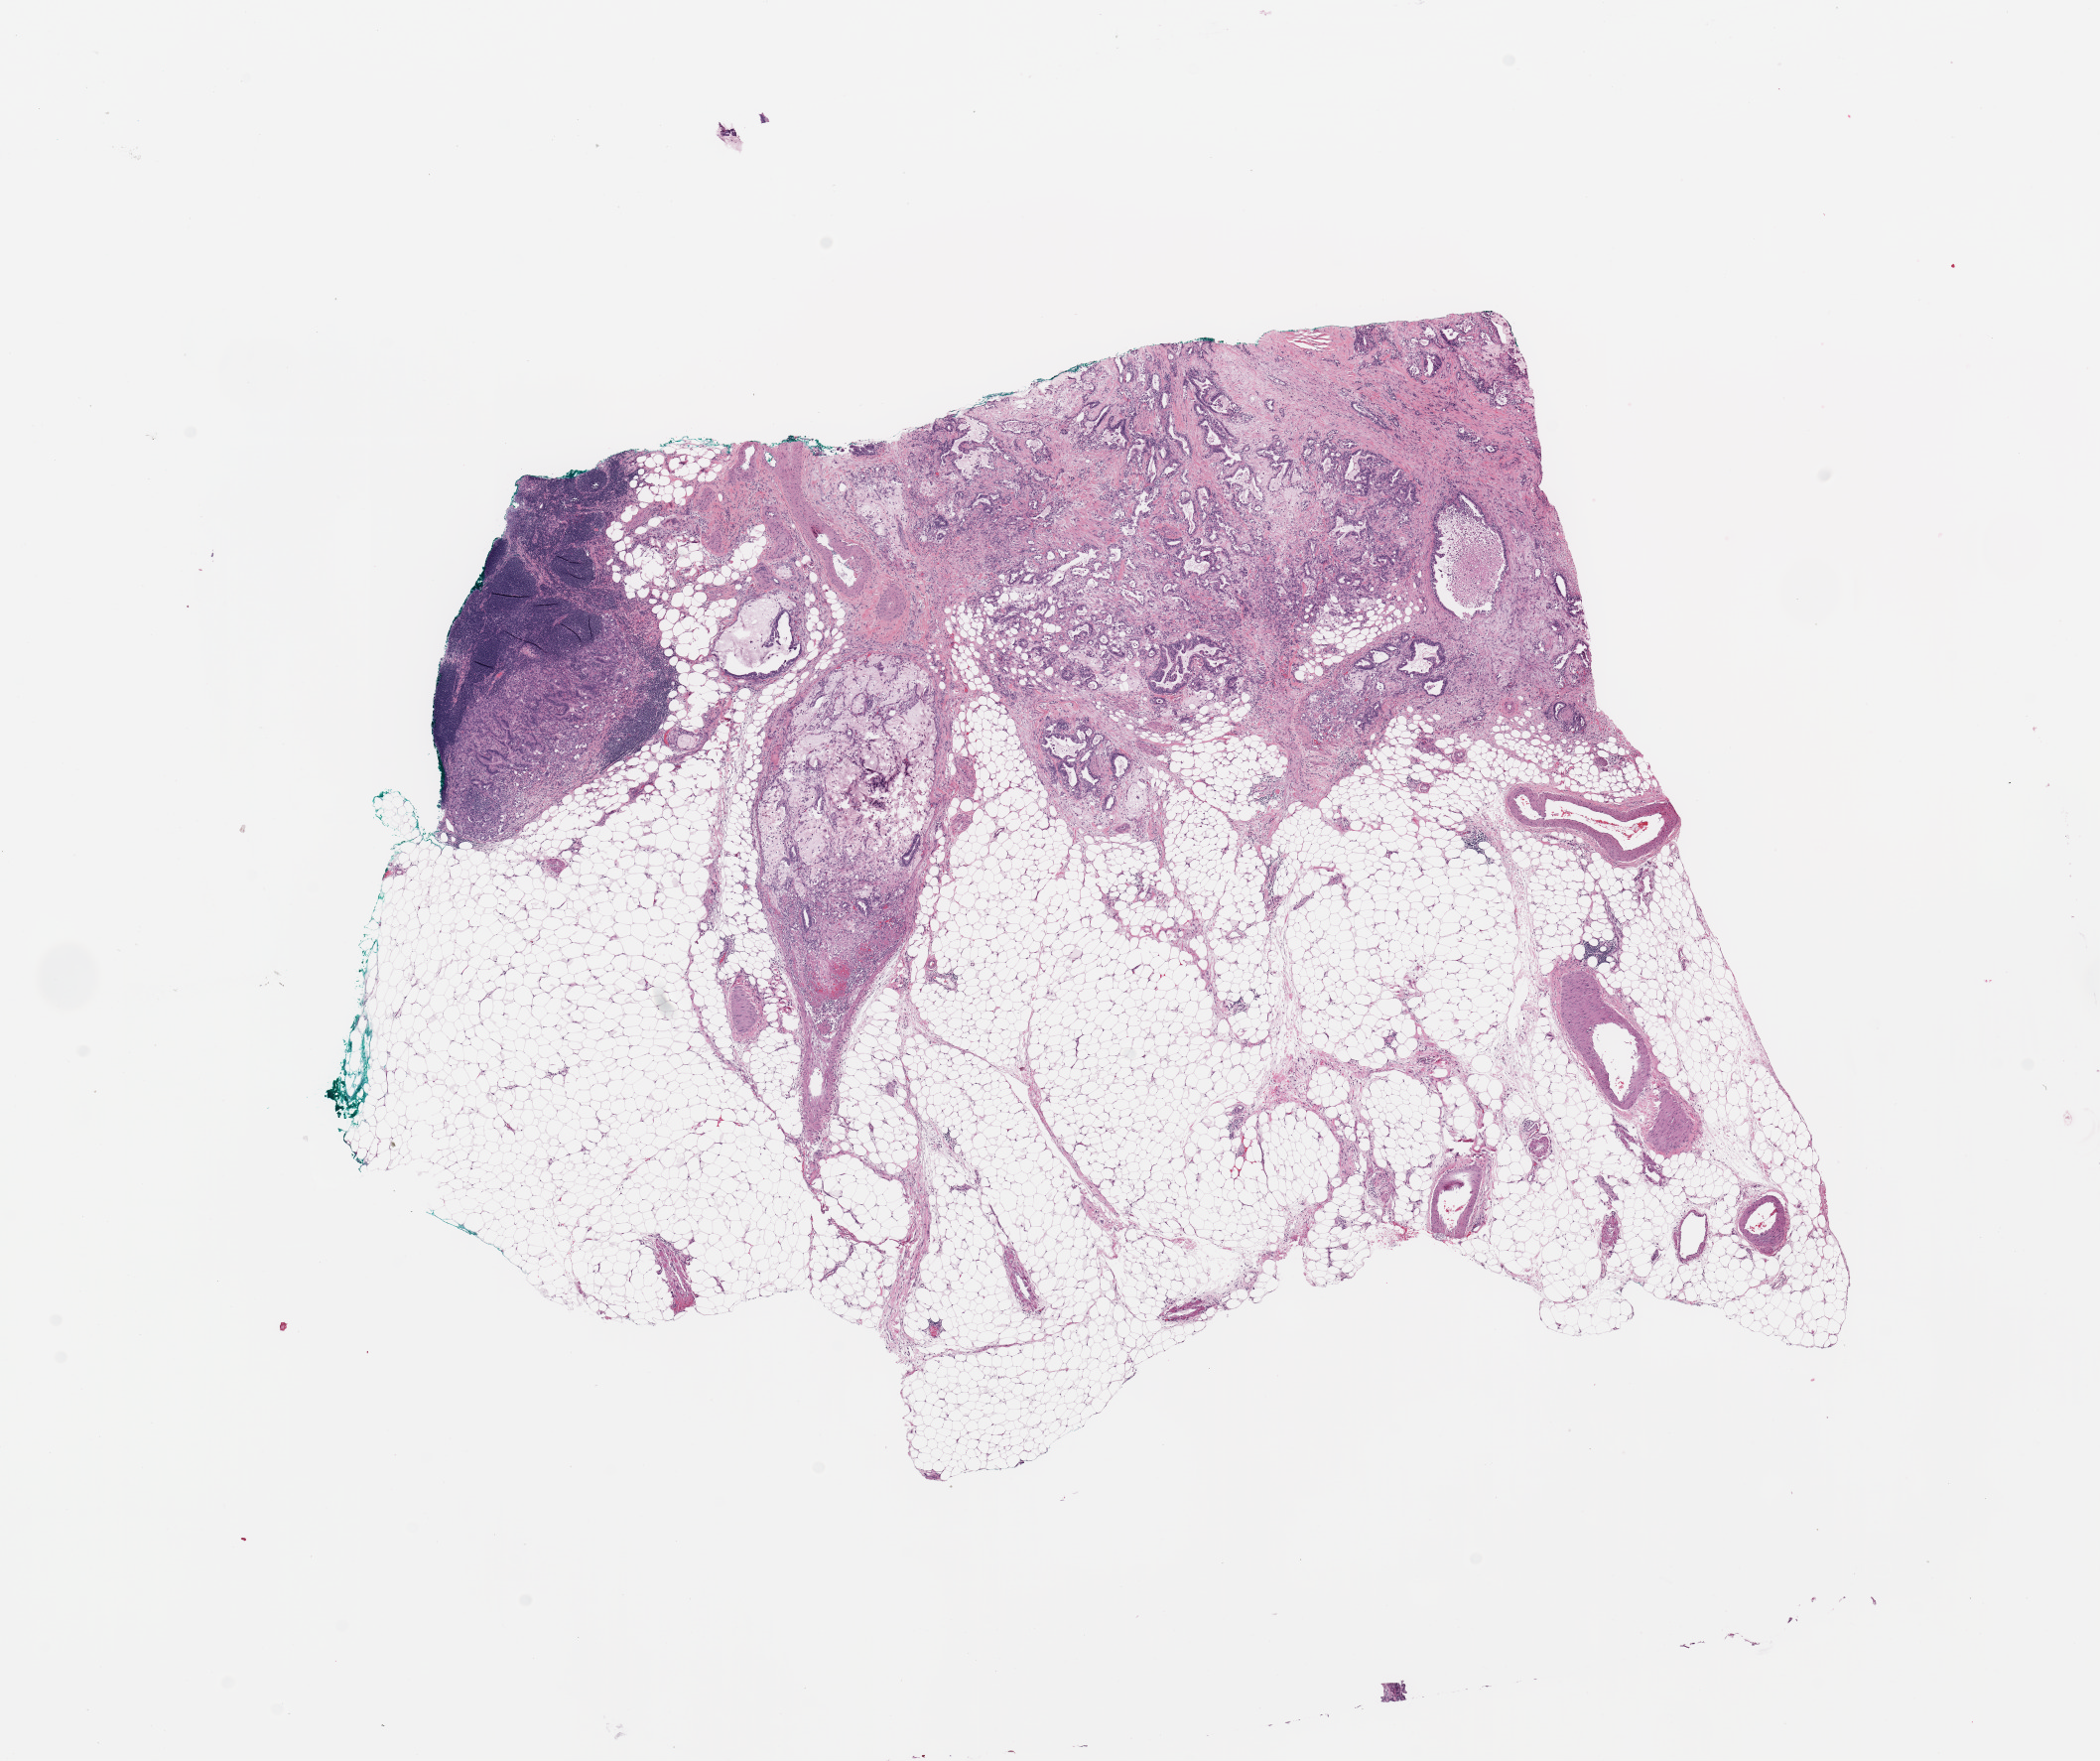
Whole-slide histology image, H&E-stained, a low-resolution overview of the entire scanned area, about 16.7 x 14.0 mm. Tumour tissue sample, pancreas. 60-year-old male patient. Histologic grade: G2 (moderately differentiated).
• primary tumour site (as recorded): head
• AJCC pathologic stage: IIB
• histologic diagnosis: Infiltrating duct carcinoma, NOS